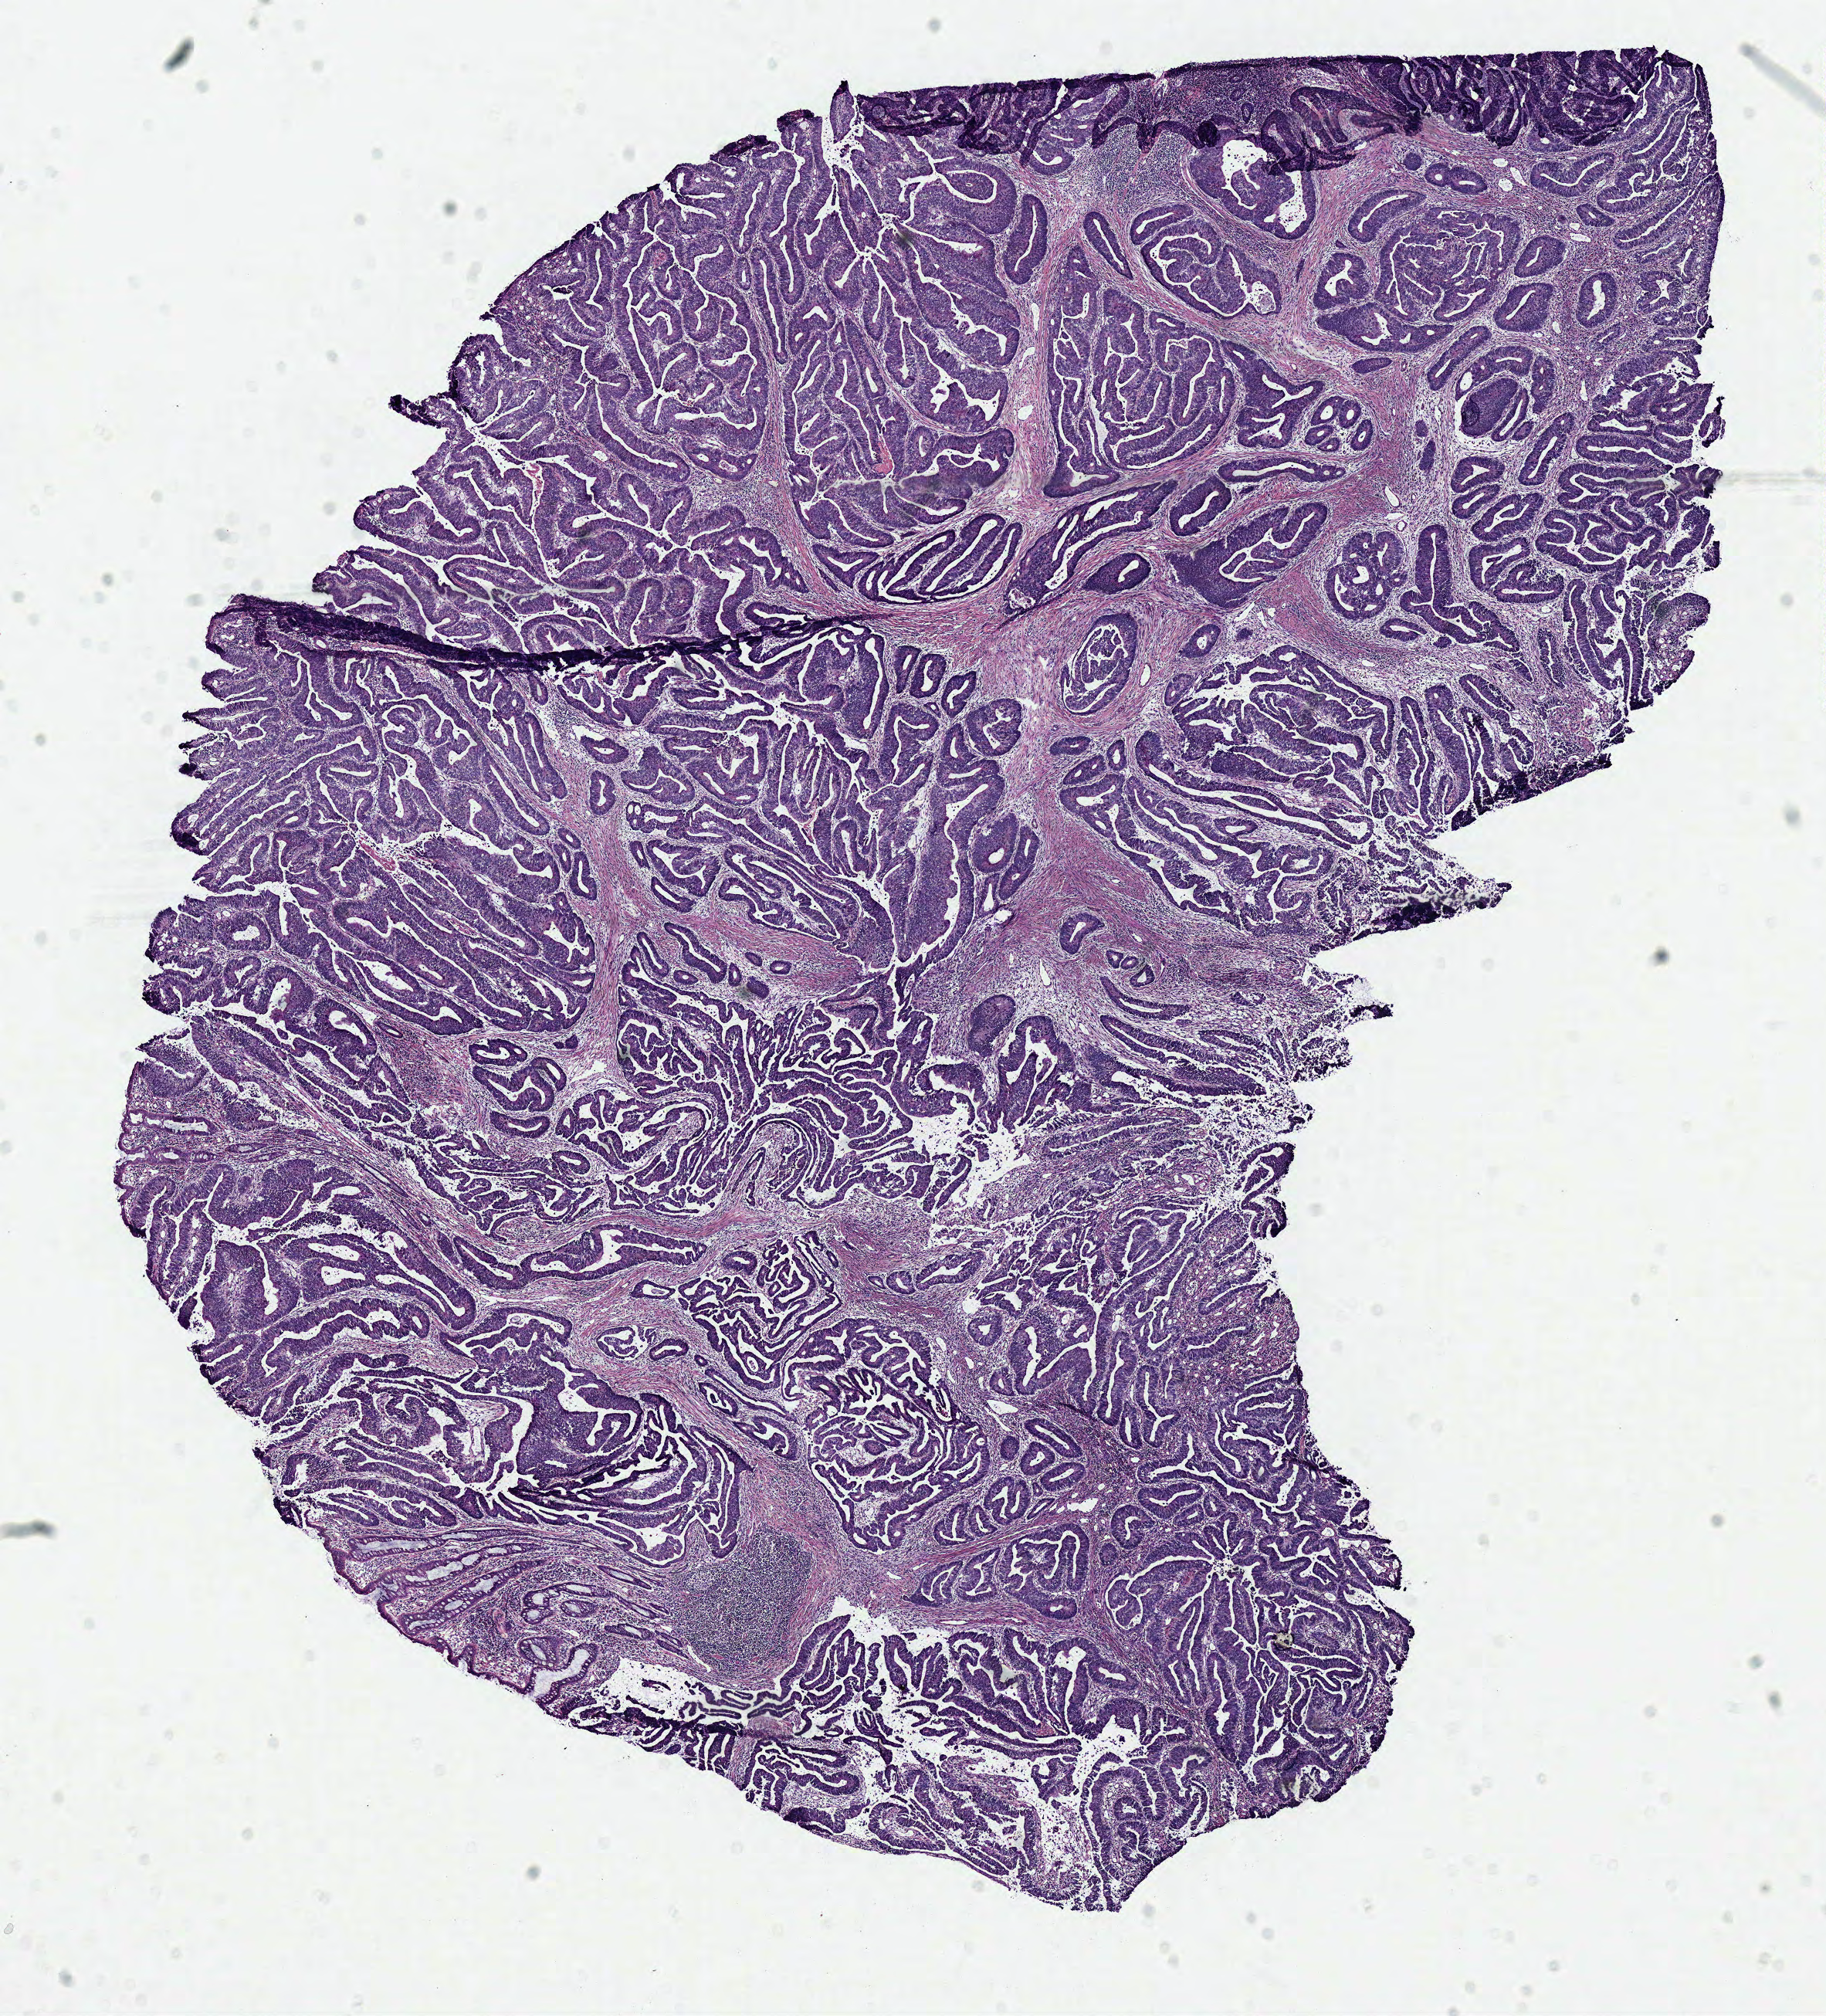
H&E-stained whole-slide image — a low-resolution overview of the entire scanned area, about 9.3 x 10.3 mm; frozen section from the top of the tissue portion; sample: primary tumour, colon. Female patient; age at initial diagnosis 37 years. Composition of this section per pathologist review: tumour cells 78%, tumour nuclei 80%, normal cells 5%, stromal cells 12%, necrosis 5%.
- lymph nodes positive (case pathology): 2 of 17 examined
- diagnosis: Adenocarcinoma, NOS (sigmoid colon)
- AJCC pathologic stage: IIIB (2nd edition)